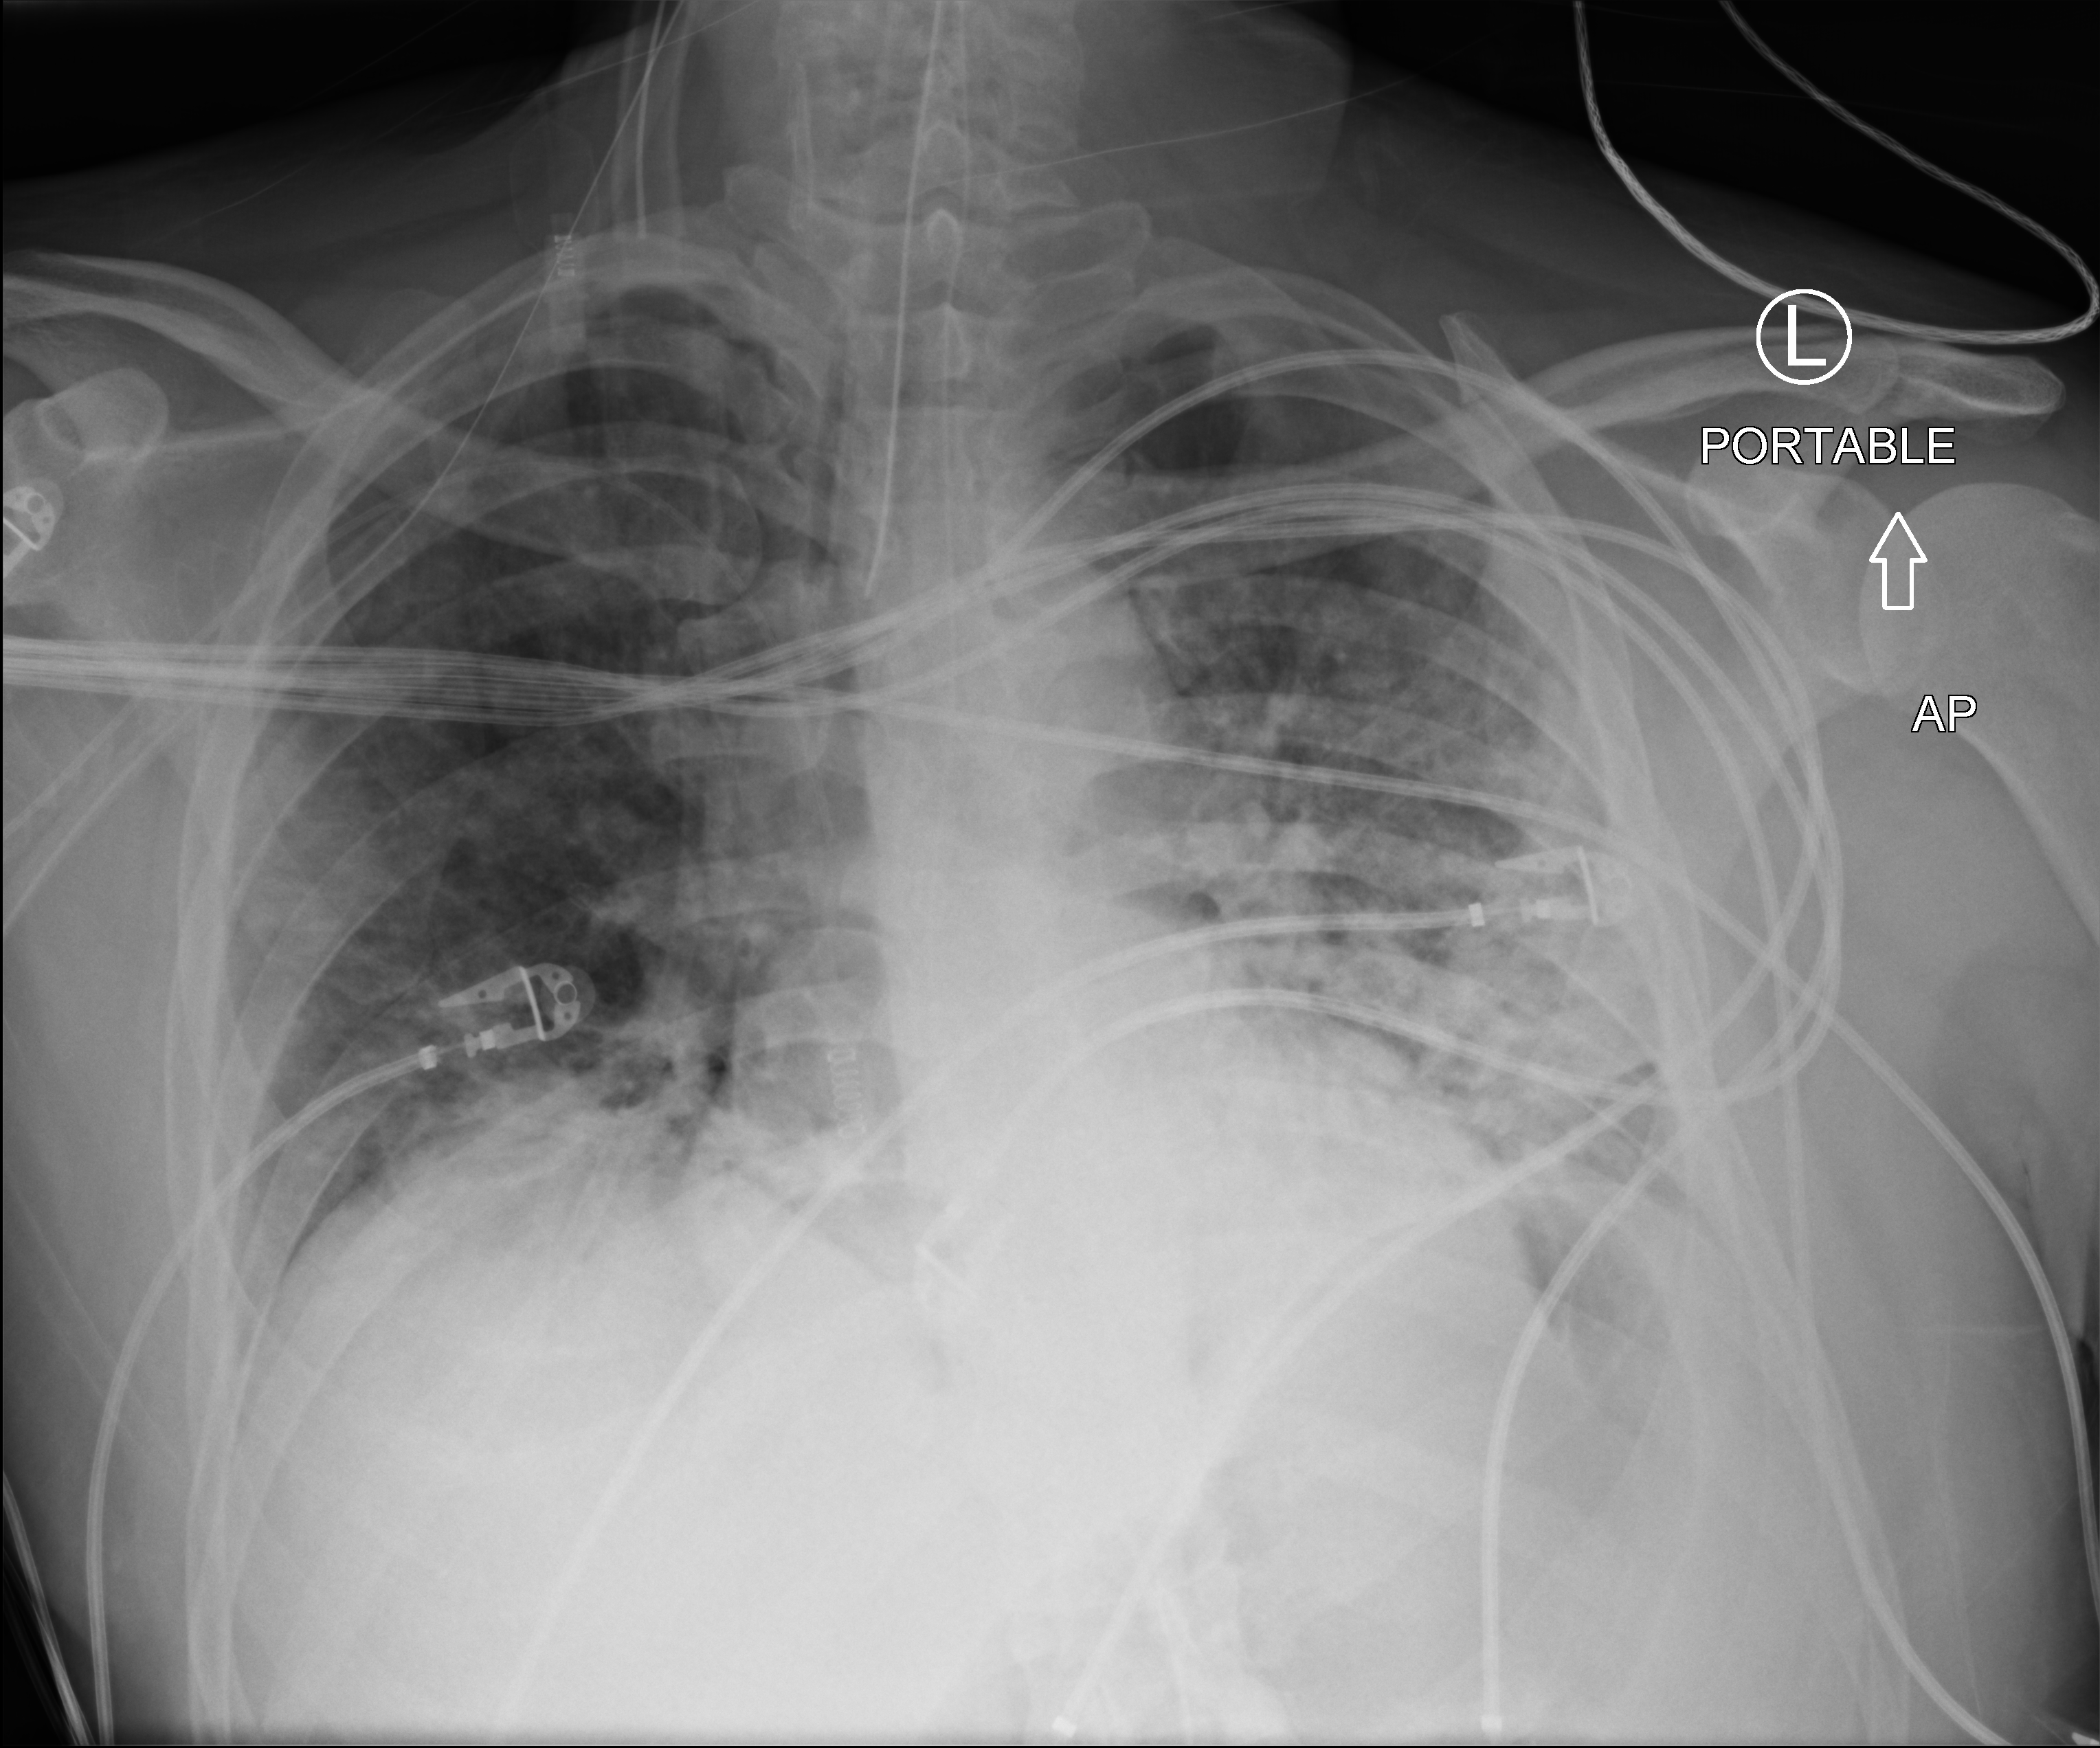
Bedside chest radiograph (computed radiography), anteroposterior (AP) projection. Male patient hospitalised with COVID-19, age 18–59 years.
Admission-level facts for this patient (not findings on this image; timing relative to this image not recorded): length of hospital stay: 15 days; mechanically ventilated during this hospital stay: yes.